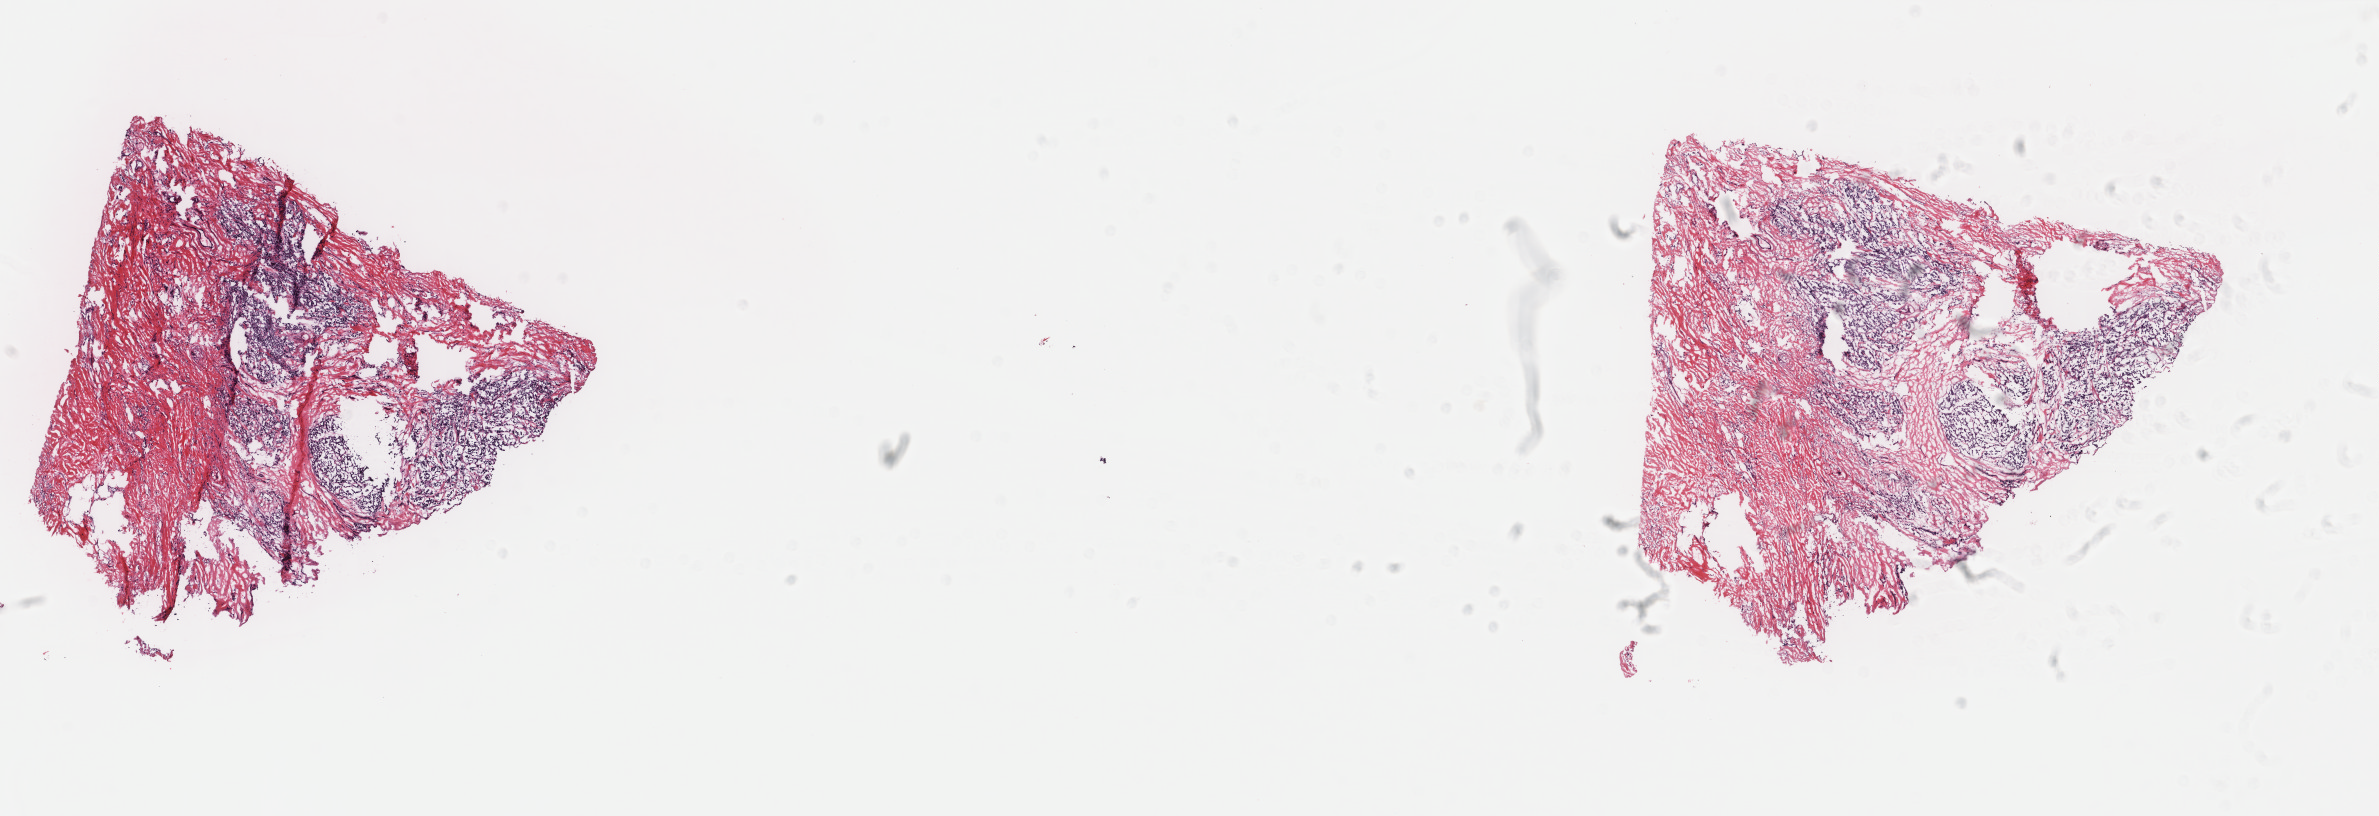
H&E whole-slide image, a low-resolution overview of the entire scanned area, about 18.9 x 6.5 mm (slide scanned at 40x), frozen section from the top of the tissue portion, primary tumour sample from the breast. Female patient; age at initial diagnosis 62 years. Composition of this section per pathologist review: tumour cells 60%, tumour nuclei 70%, normal cells 0%, stromal cells 40%, necrosis 0%. Inflammatory infiltration, as recorded: lymphocyte infiltration 0%, monocyte infiltration 0%, neutrophil infiltration 0%.
• lymph nodes positive (case pathology): 0 of 28 examined
• laterality: right
• pathologic diagnosis: Lobular carcinoma, NOS
• AJCC pathologic stage: IIA (5th edition)